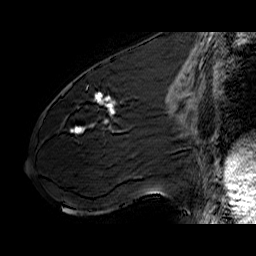
Breast MRI (dynamic contrast-enhanced), one sagittal slice; position 28 of 60 along the scan axis; dynamic contrast-enhanced series, time point 2 of 6 at this slice position (early post-contrast); 1.5 T; TE 6.4 ms, TR 32.9 ms; 256 × 256 image matrix, field of view 200 × 200 mm. Female patient. From the clinical record (not read from this slice): setting: breast cancer imaged before/during neoadjuvant chemotherapy; receptor status: HER2-positive.
Structures marked on this image (semi-automatically segmented with operator editing):
- analysis volume of interest (the breast-tissue region the enhancement analysis was run in; not a lesion): bounding box <61,77,141,142> (left, top, right, bottom; pixels)
- tumour enhancement mask (voxels above the 100 % enhancement threshold inside the analysis volume of interest): <70,92,116,133>